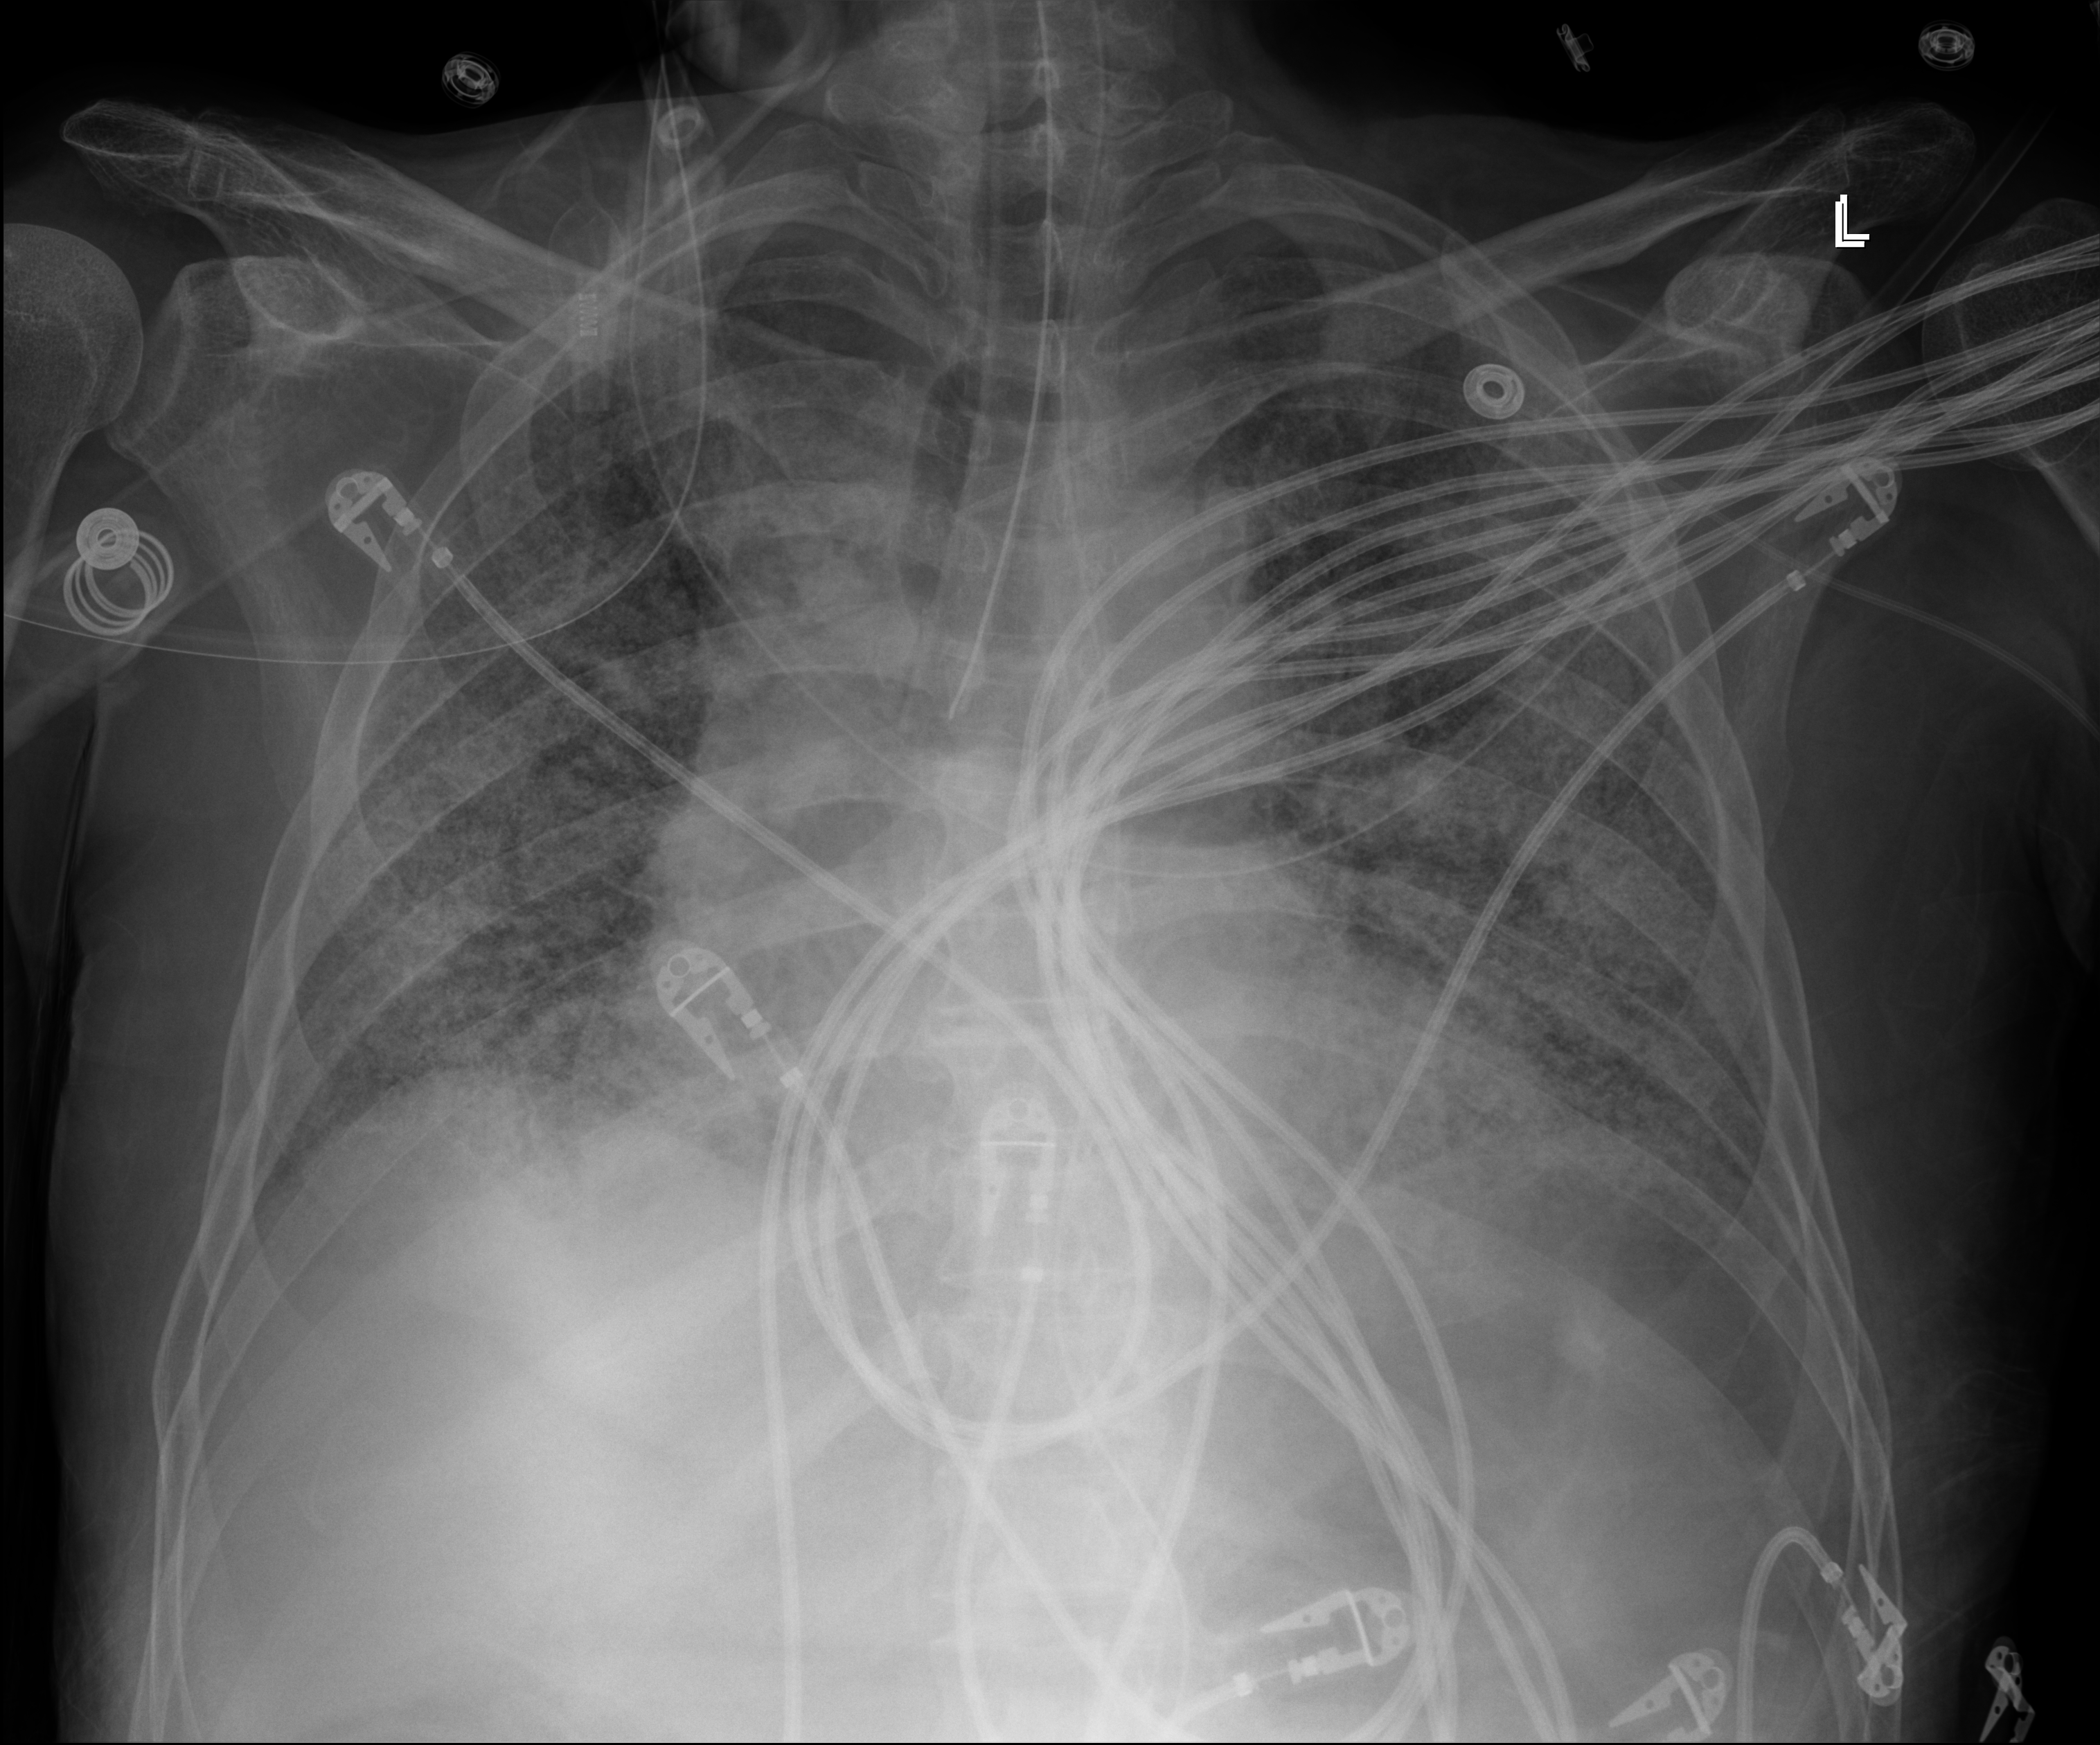
Chest X-ray (portable); anteroposterior (AP) projection. Male patient hospitalised with COVID-19, age 60–74 years.
From the hospital-stay record, not from the radiograph (when in the stay this image was taken is not recorded):
- mechanically ventilated during this hospital stay: yes